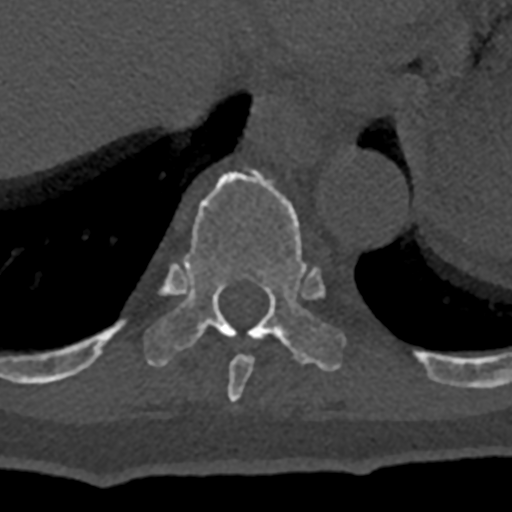
CT including the spine, one axial slice. Slice 614 of 797 in the series (ordered by position). Reconstruction kernel Br40s/3. Bone window (W 1800 / L 400 HU). 0.5 mm slice thickness. 512 × 512 image matrix, field of view 160 × 160 mm. Male patient, age 74 years. Case-level facts recorded for this patient, not image findings: primary cancer: renal.
Structures marked on this image (semi-automatically segmented with operator editing):
- T10 vertebra: bounding box [x1, y1, x2, y2] px = [70, 169, 432, 378]
- T9 vertebra: [227, 354, 253, 403]